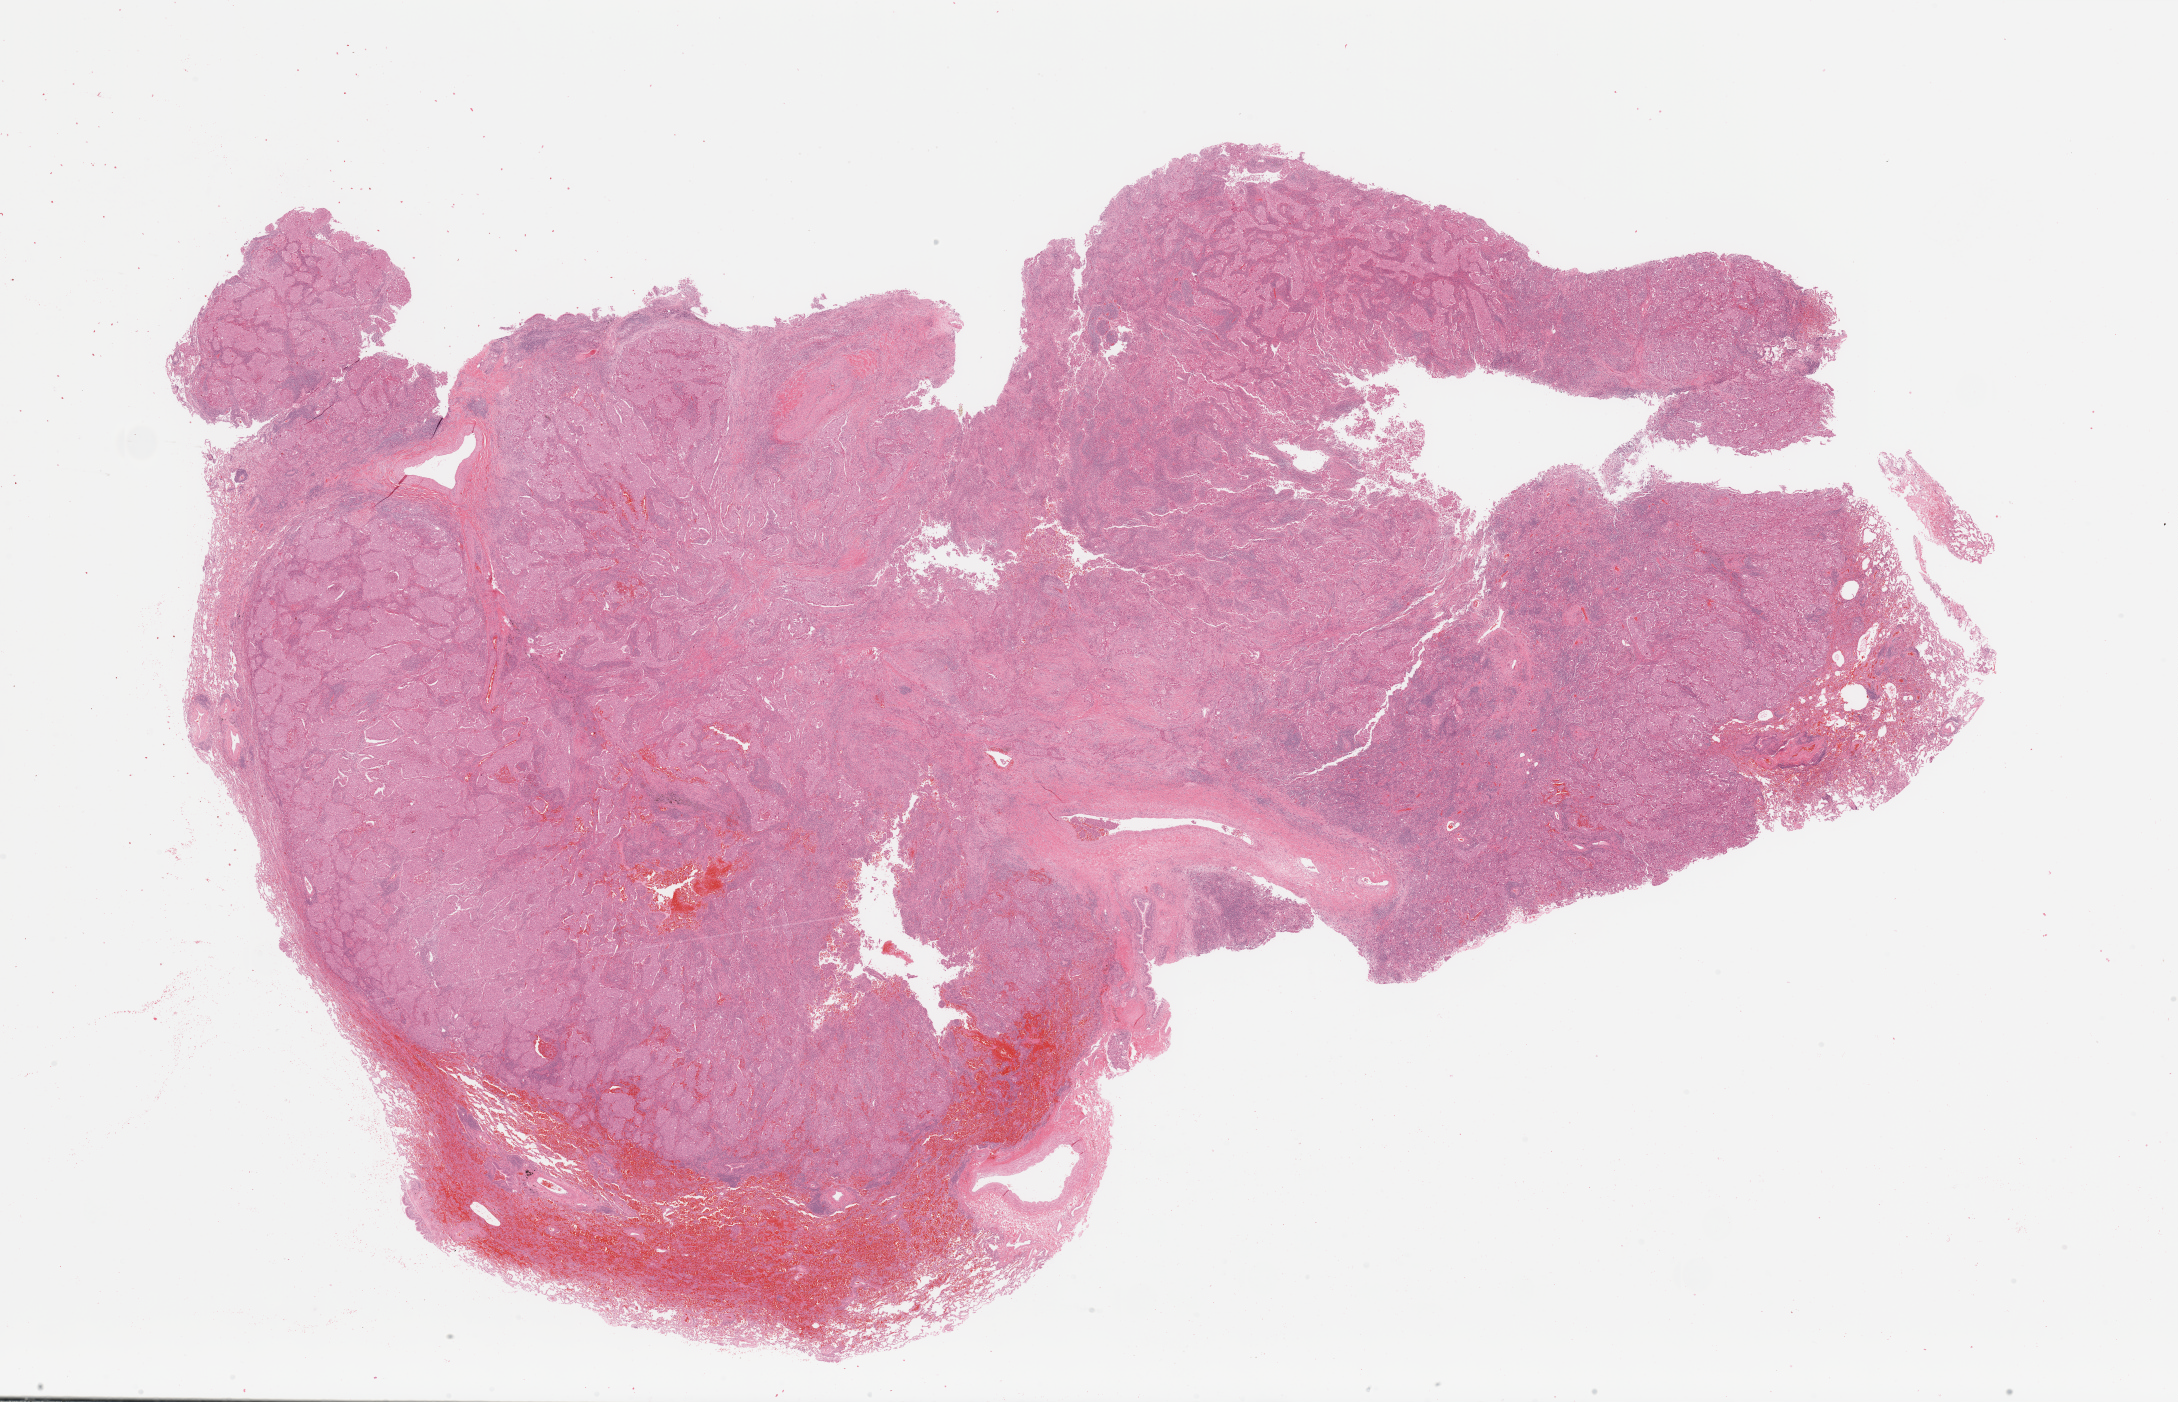
H&E whole-slide image — shown as a low-resolution overview of the whole scanned area (about 34.5 x 22.2 mm). Lung, tumour tissue. Patient: female, age 48 years. Histologic grade: G3 (poorly differentiated).
- AJCC pathologic stage: IIA
- diagnosis: Adenocarcinoma, NOS